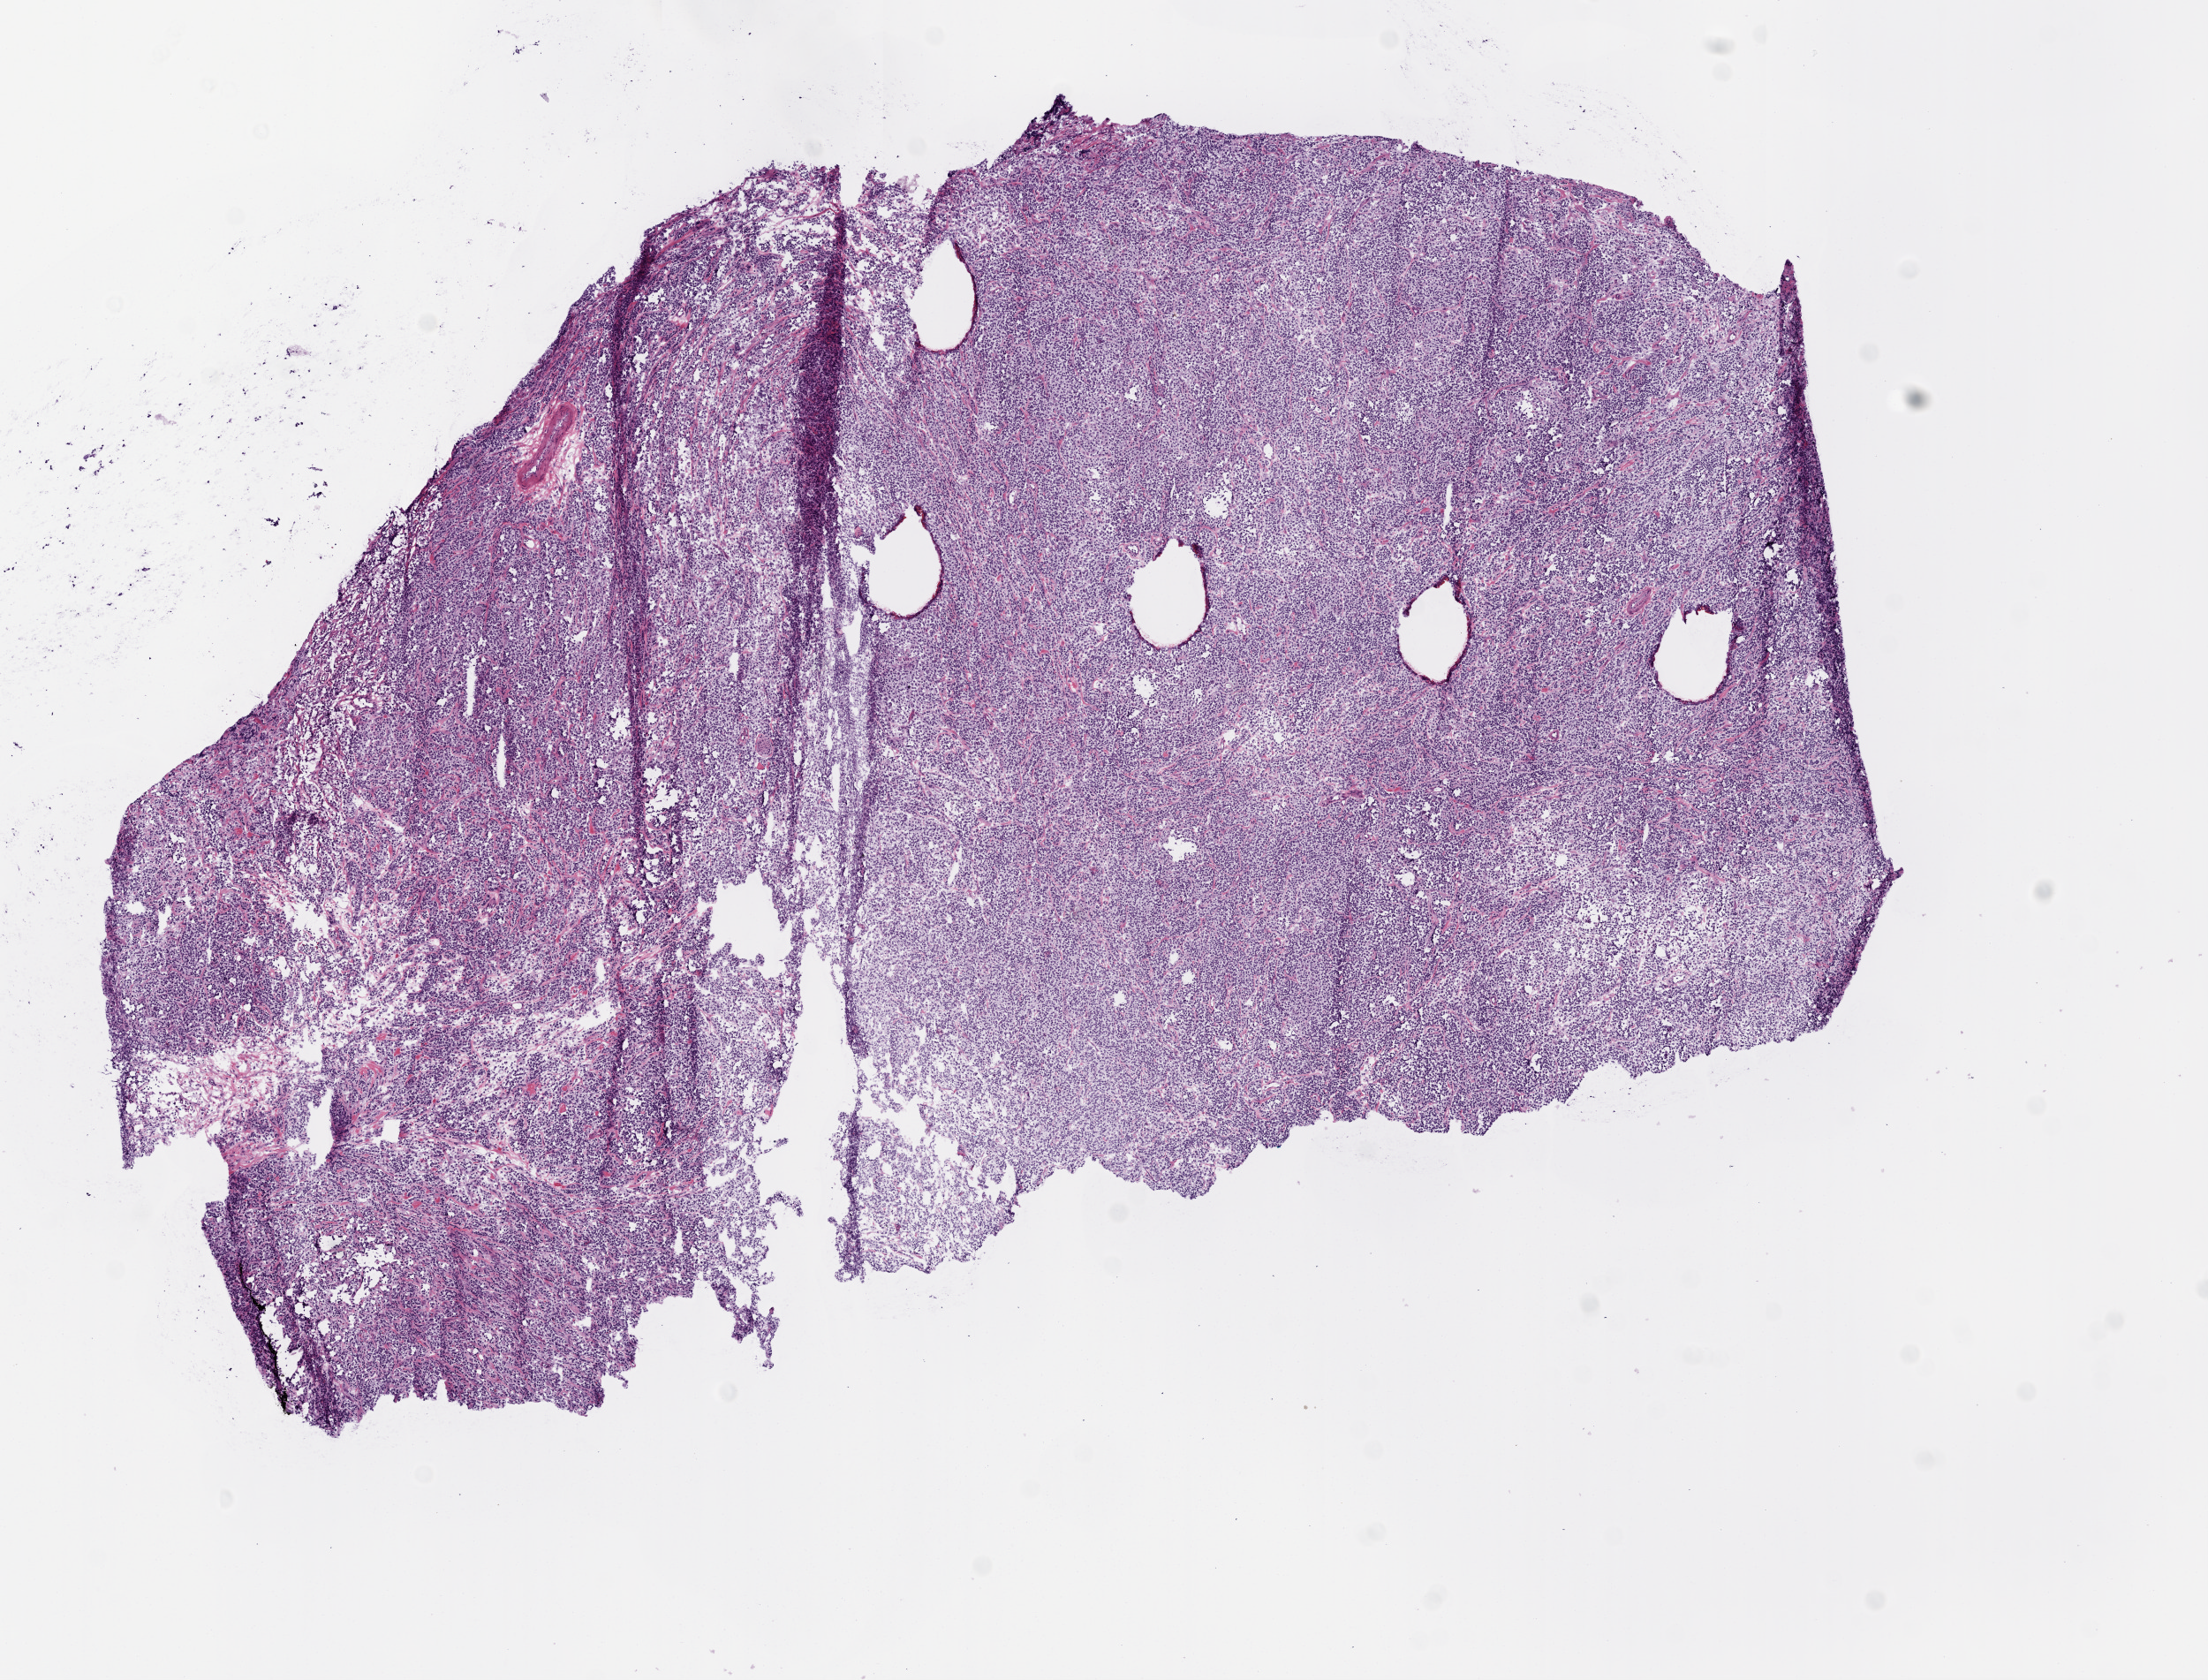
Digitized H&E tissue section (whole slide) — a low-resolution overview of the entire scanned area, about 10.0 x 7.6 mm (slide scanned at 20x), frozen section from the top of the tissue portion, sample: primary tumour, lymphoid tissue. Female patient; age at initial diagnosis 70 years. Composition of this section per pathologist review: tumour cells 90%, tumour nuclei 75%, normal cells 0%, stromal cells 10%, necrosis 0%.
* pathologic diagnosis: Diffuse large B-cell lymphoma, NOS